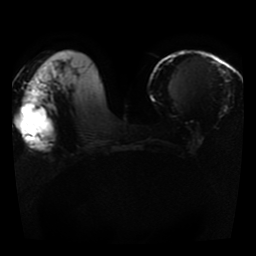
Breast MRI, one axial slice; slice 13 of 41 in the series (ordered by position); diffusion-weighted series; image 2 of 4 stored at this slice position (different b-values; order by instance number); 1.5 T; 5 mm slice thickness; 256 × 256 image matrix, field of view 330 × 330 mm. Female patient.
Structures marked on this image (manually delineated by an expert):
- tumour on diffusion-weighted imaging: bounding box <29,88,47,104> (left, top, right, bottom; pixels)